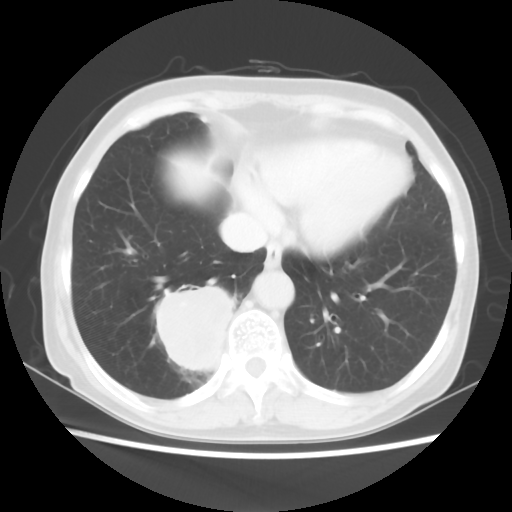
Chest CT, one axial slice; slice 16 of 56 in the series (ordered by position); reconstruction kernel STANDARD; 120 kVp; lung window (W 1500 / L -600 HU); 5 mm slice thickness; 512 × 512 image matrix, field of view 332 × 332 mm. Female patient, age 66 years. Case-level facts recorded for this patient, not image findings: clinical TNM (as recorded): T2 N3 M0.
Outlined on this slice (bounding box drawn by a radiologist):
- lung tumour (recorded histology: small cell carcinoma): bounding box <157,277,237,380> (left, top, right, bottom; pixels)